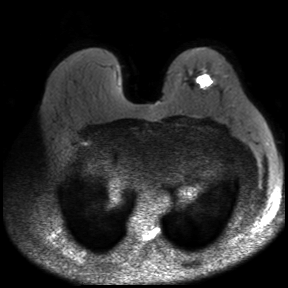
Breast MRI, one axial slice; slice 23 of 30 in the series (ordered by position); diffusion-weighted series; image 2 of 4 stored at this slice position (different b-values; order by instance number); 3 T; 4 mm slice thickness; 288 × 288 image matrix. Female patient.
Structures marked on this image (expert manual segmentation):
- tumour on diffusion-weighted imaging: bounding box [x1, y1, x2, y2] px = [198, 75, 211, 85]